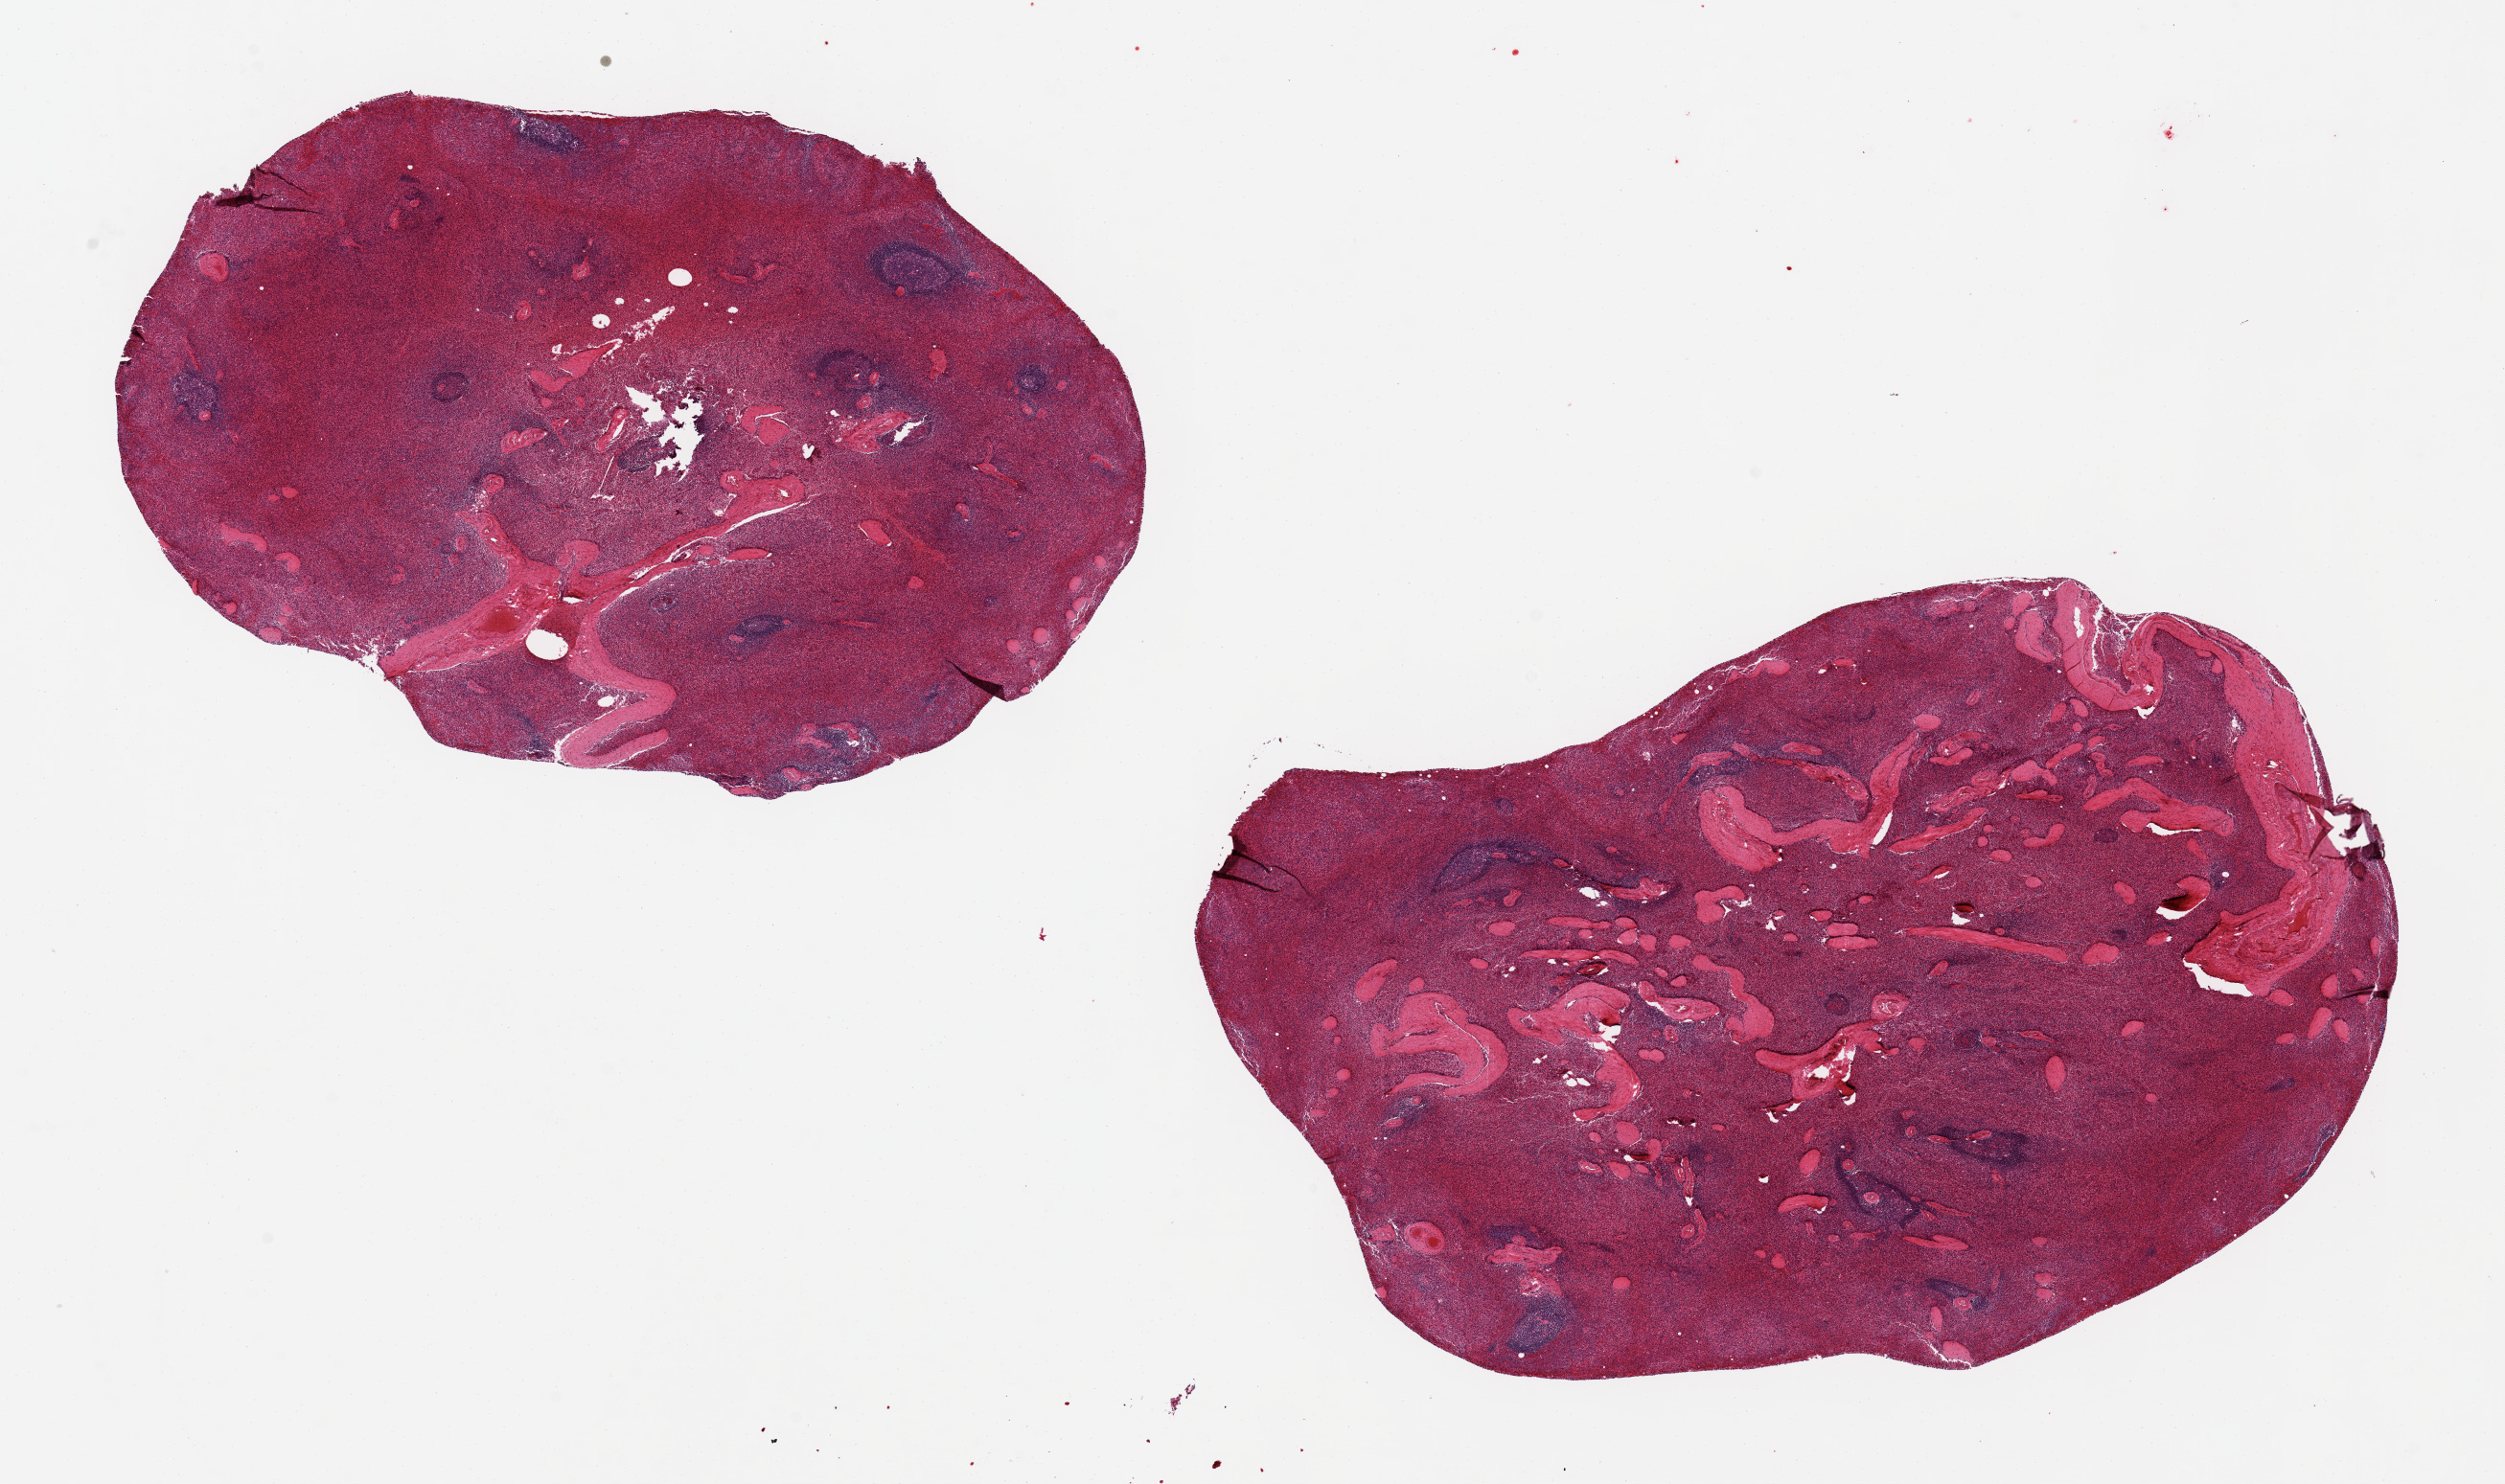
Digitized H&E-stained section, brightfield, shown as a low-resolution overview of the whole scanned area (about 20.7 x 12.3 mm, acquisition: 20x scan). PAXgene-fixed, paraffin-embedded tissue. Sampled site (target tissue): spleen. Tissue donor sample.
- review note (as recorded): 2 ~8.5x6mm aliquots; red pulp markedly congested